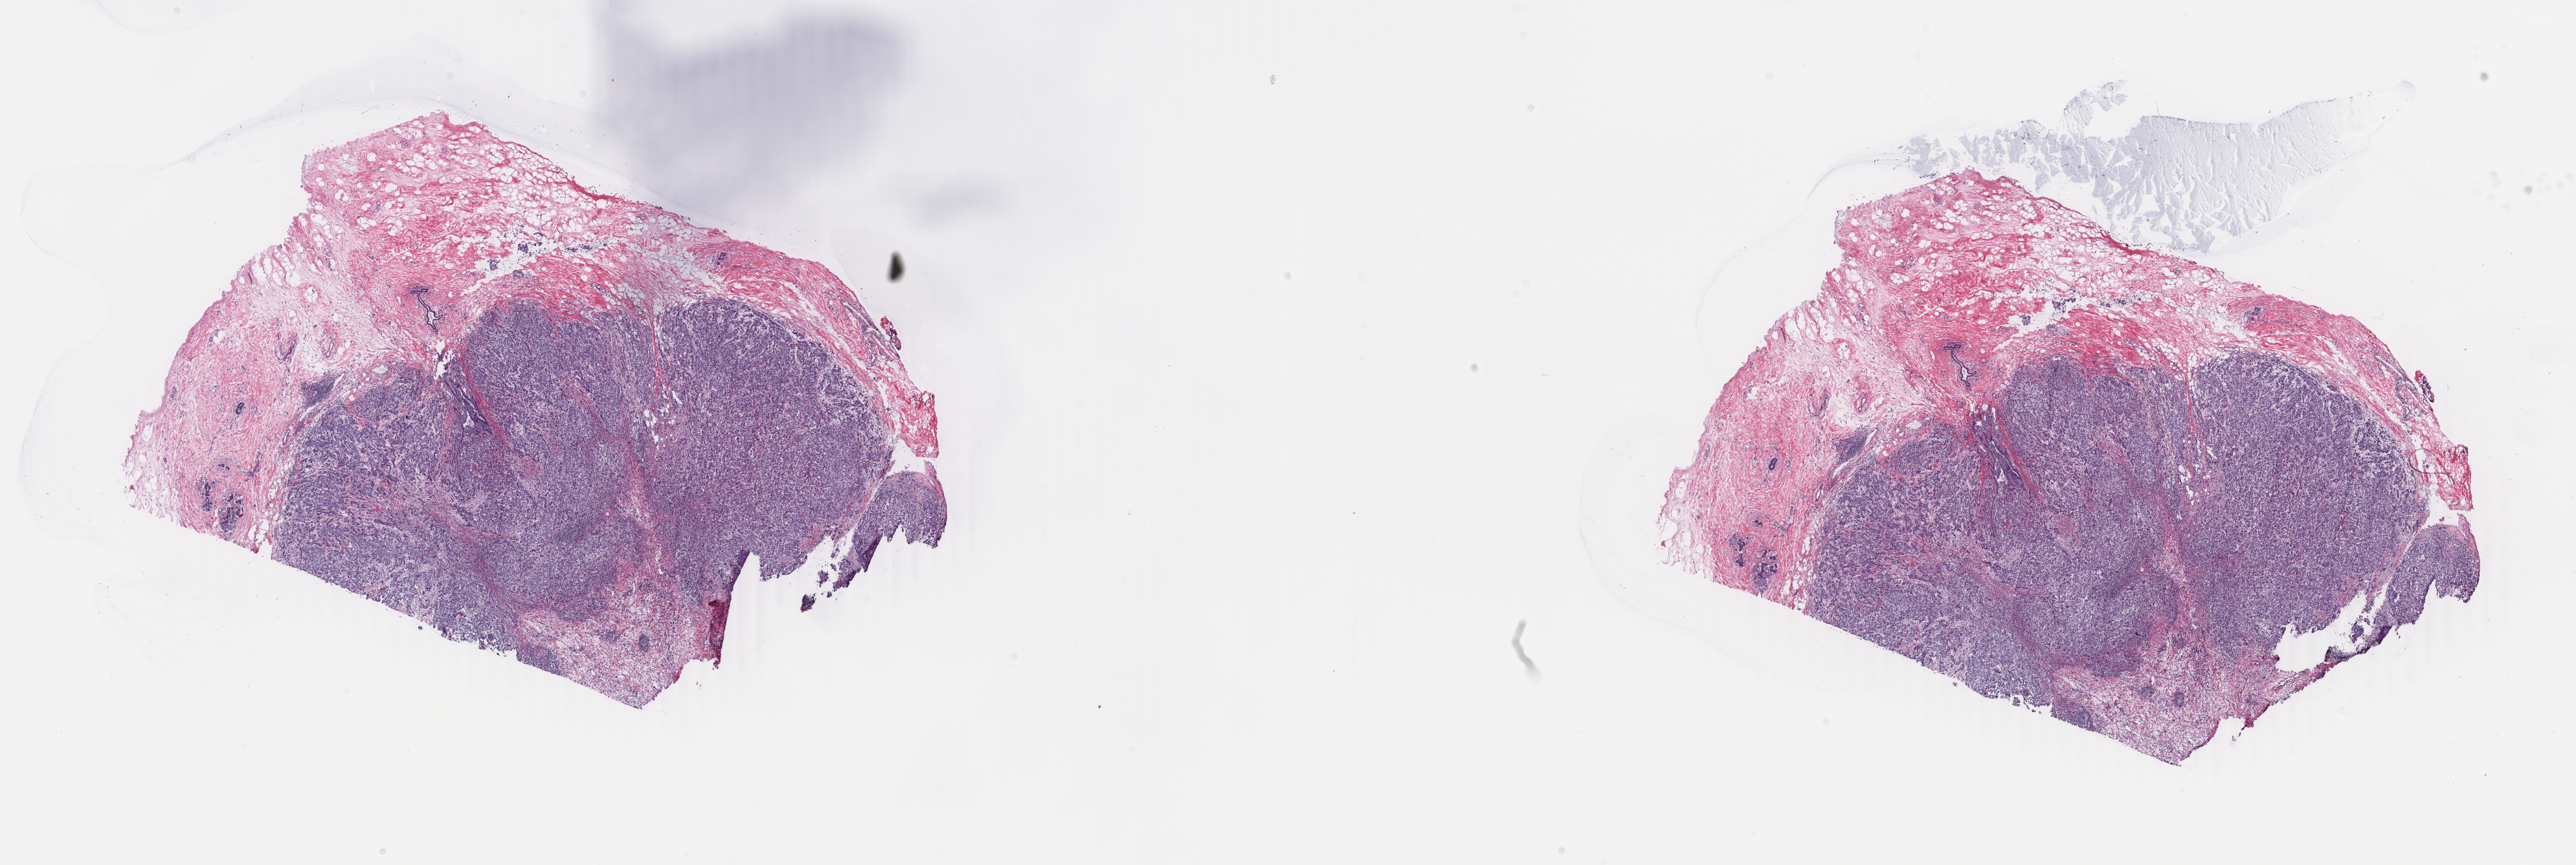
Digitized H&E-stained tissue section (whole slide), shown as a low-resolution overview of the whole scanned area (about 31.6 x 10.6 mm, acquisition: 40x scan); frozen section from the top of the tissue portion; primary tumour sample from the breast. Female, age 29 years at initial diagnosis. Pathologist review of this section (percent, as recorded): tumour cells 70%, tumour nuclei 70%, normal cells 2%, stromal cells 26%, necrosis 2%. Inflammatory infiltration, as recorded: lymphocyte infiltration 4%, monocyte infiltration 2%, neutrophil infiltration 1%.
- histologic diagnosis: Infiltrating duct carcinoma, NOS
- TNM: T1c N0 (i-) M0
- AJCC pathologic stage: I (6th edition)
- lymph nodes positive (case pathology): 0 of 2 examined